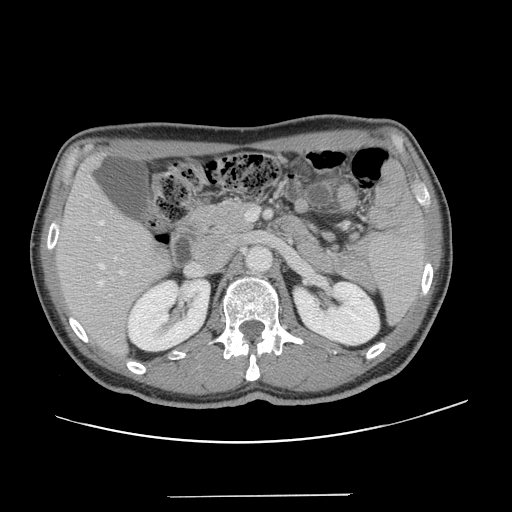
Contrast-enhanced abdominal CT, one axial slice; position 71 of 131 along the scan axis; 120 kVp; soft-tissue window (W 400 / L 40 HU); 2.5 mm slice thickness; 512 × 512 image matrix, field of view 403 × 403 mm. Male patient, age 60 years. From the clinical record (not read from this slice): diagnosis: colorectal cancer liver metastases, imaged before liver resection; multiple liver metastases: no.
Structures marked on this image (expert manual segmentation):
- hepatic veins: bounding box [x1, y1, x2, y2] px = [98, 221, 117, 286]
- liver: [57, 158, 169, 354]
- planned liver remnant (the part of the liver to remain after resection): [57, 158, 168, 354]